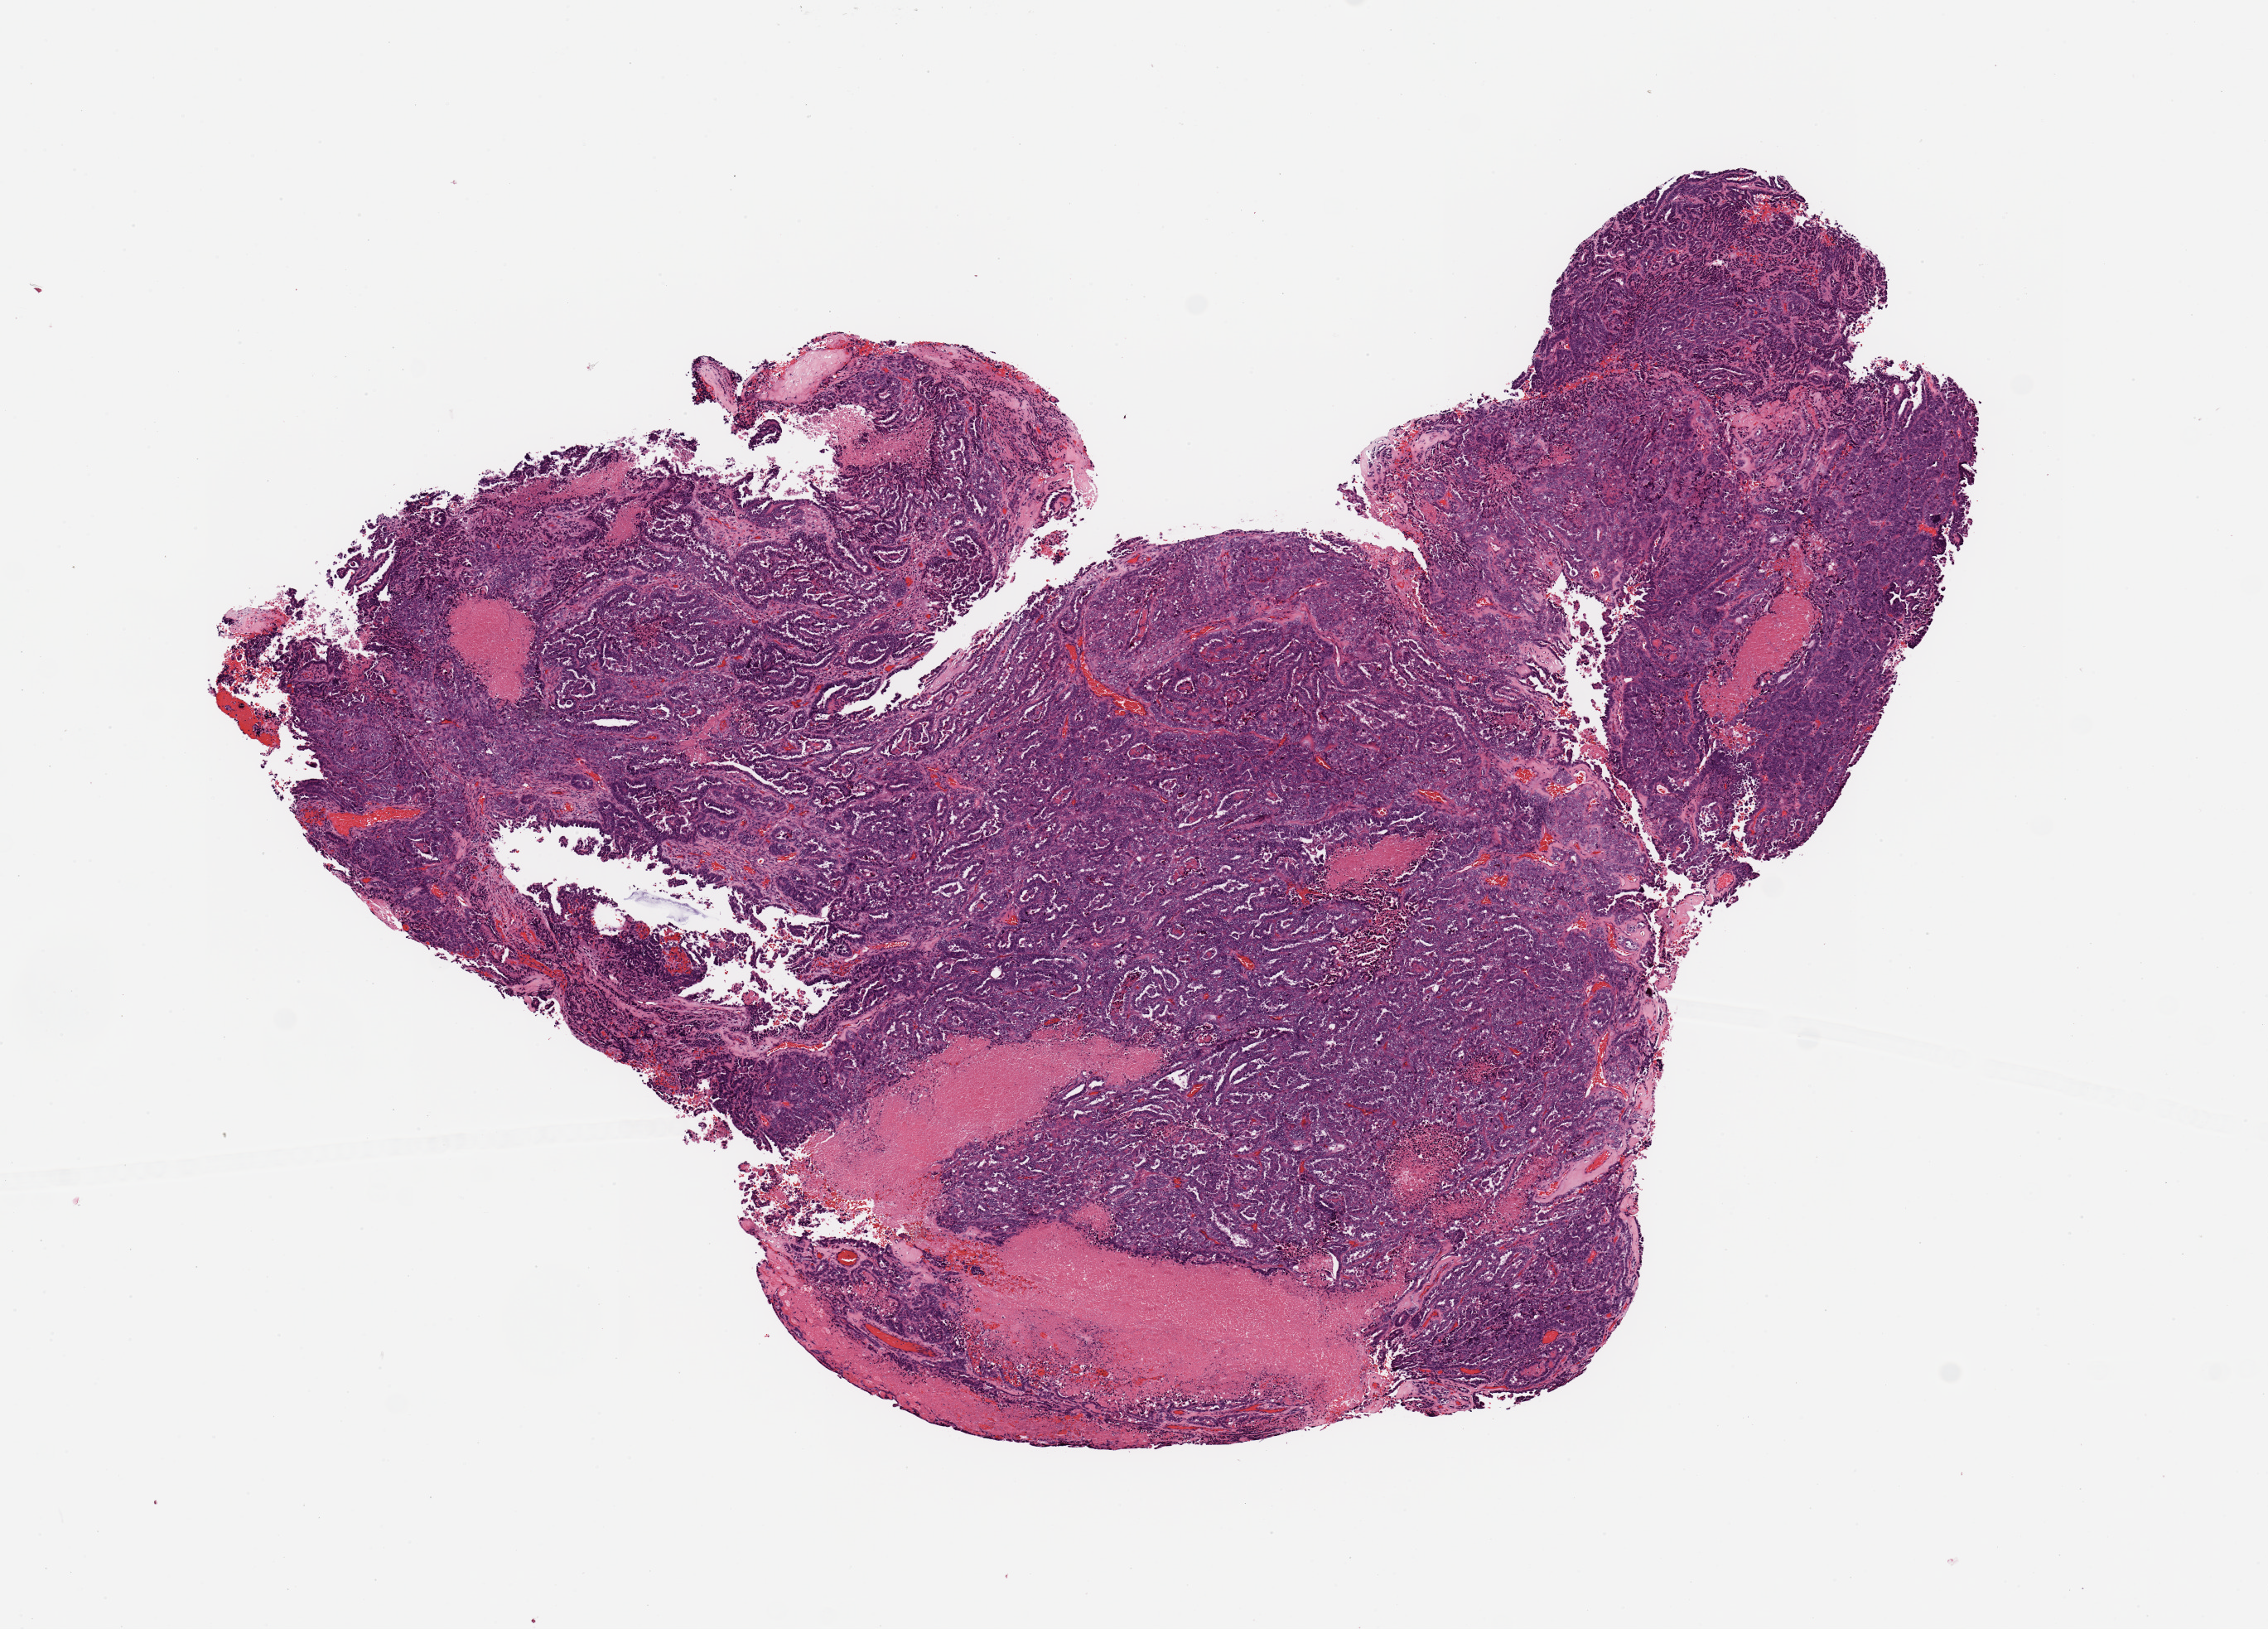
Digitized H&E tissue section (whole slide), a low-resolution overview of the entire scanned area, about 10.8 x 7.8 mm, tumour tissue sample, uterus. 73-year-old female patient.
Histologic diagnosis: Endometrioid adenocarcinoma, NOS.